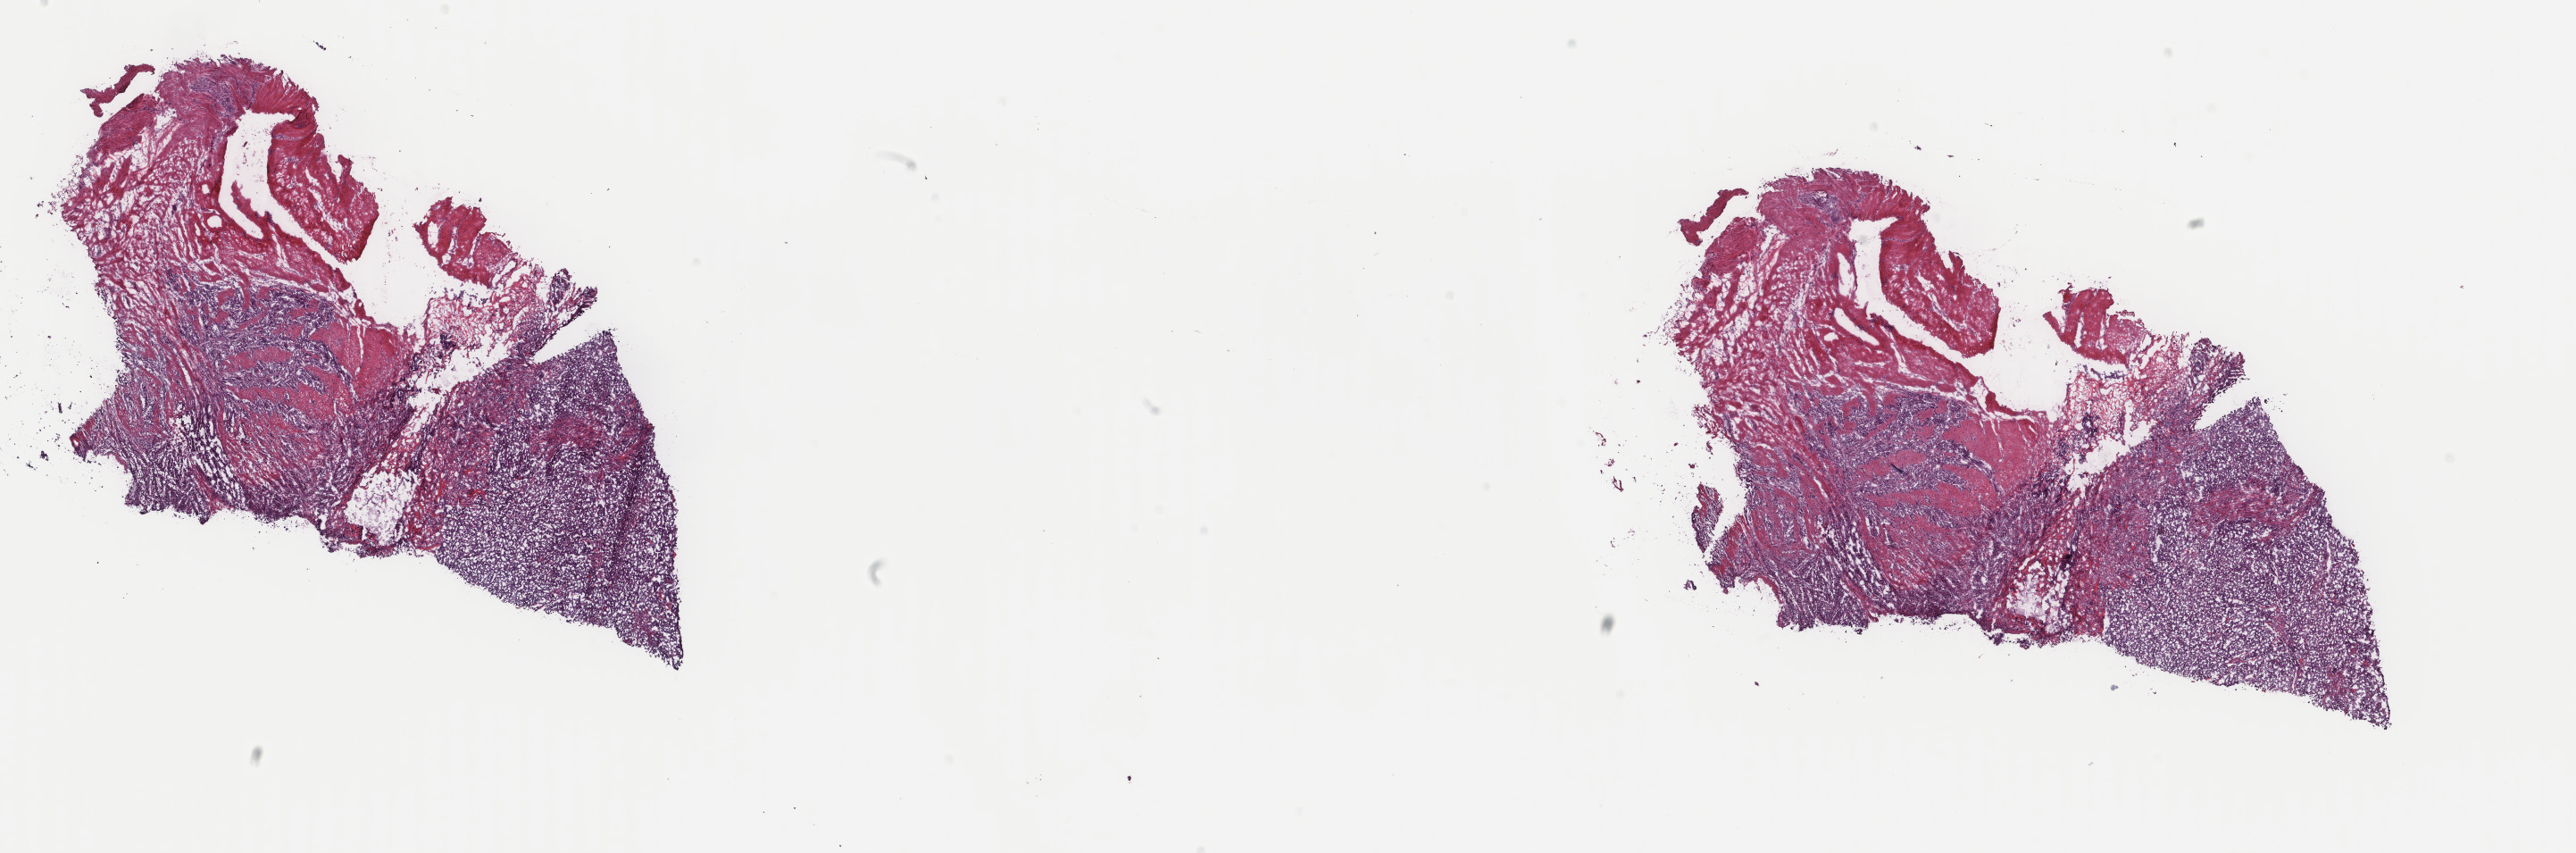
H&E-stained whole-slide image — low-resolution overview of the scanned area, about 22.9 x 7.6 mm, frozen section from the top of the tissue portion, sample: primary tumour, stomach. Patient: male, age at initial diagnosis 51 years. Histologic grade: G3 (poorly differentiated). Composition of this section per pathologist review: tumour cells 80%, tumour nuclei 80%, normal cells 20%, stromal cells 0%, necrosis 0%. Inflammatory infiltration, as recorded: lymphocyte infiltration 1%, monocyte infiltration 0%, neutrophil infiltration 0%.
Lymph nodes positive (case pathology): 1 of 2 examined. Histologic diagnosis: Carcinoma, diffuse type (gastric antrum). AJCC pathologic stage: IIB. TNM: T3 N1 M0.